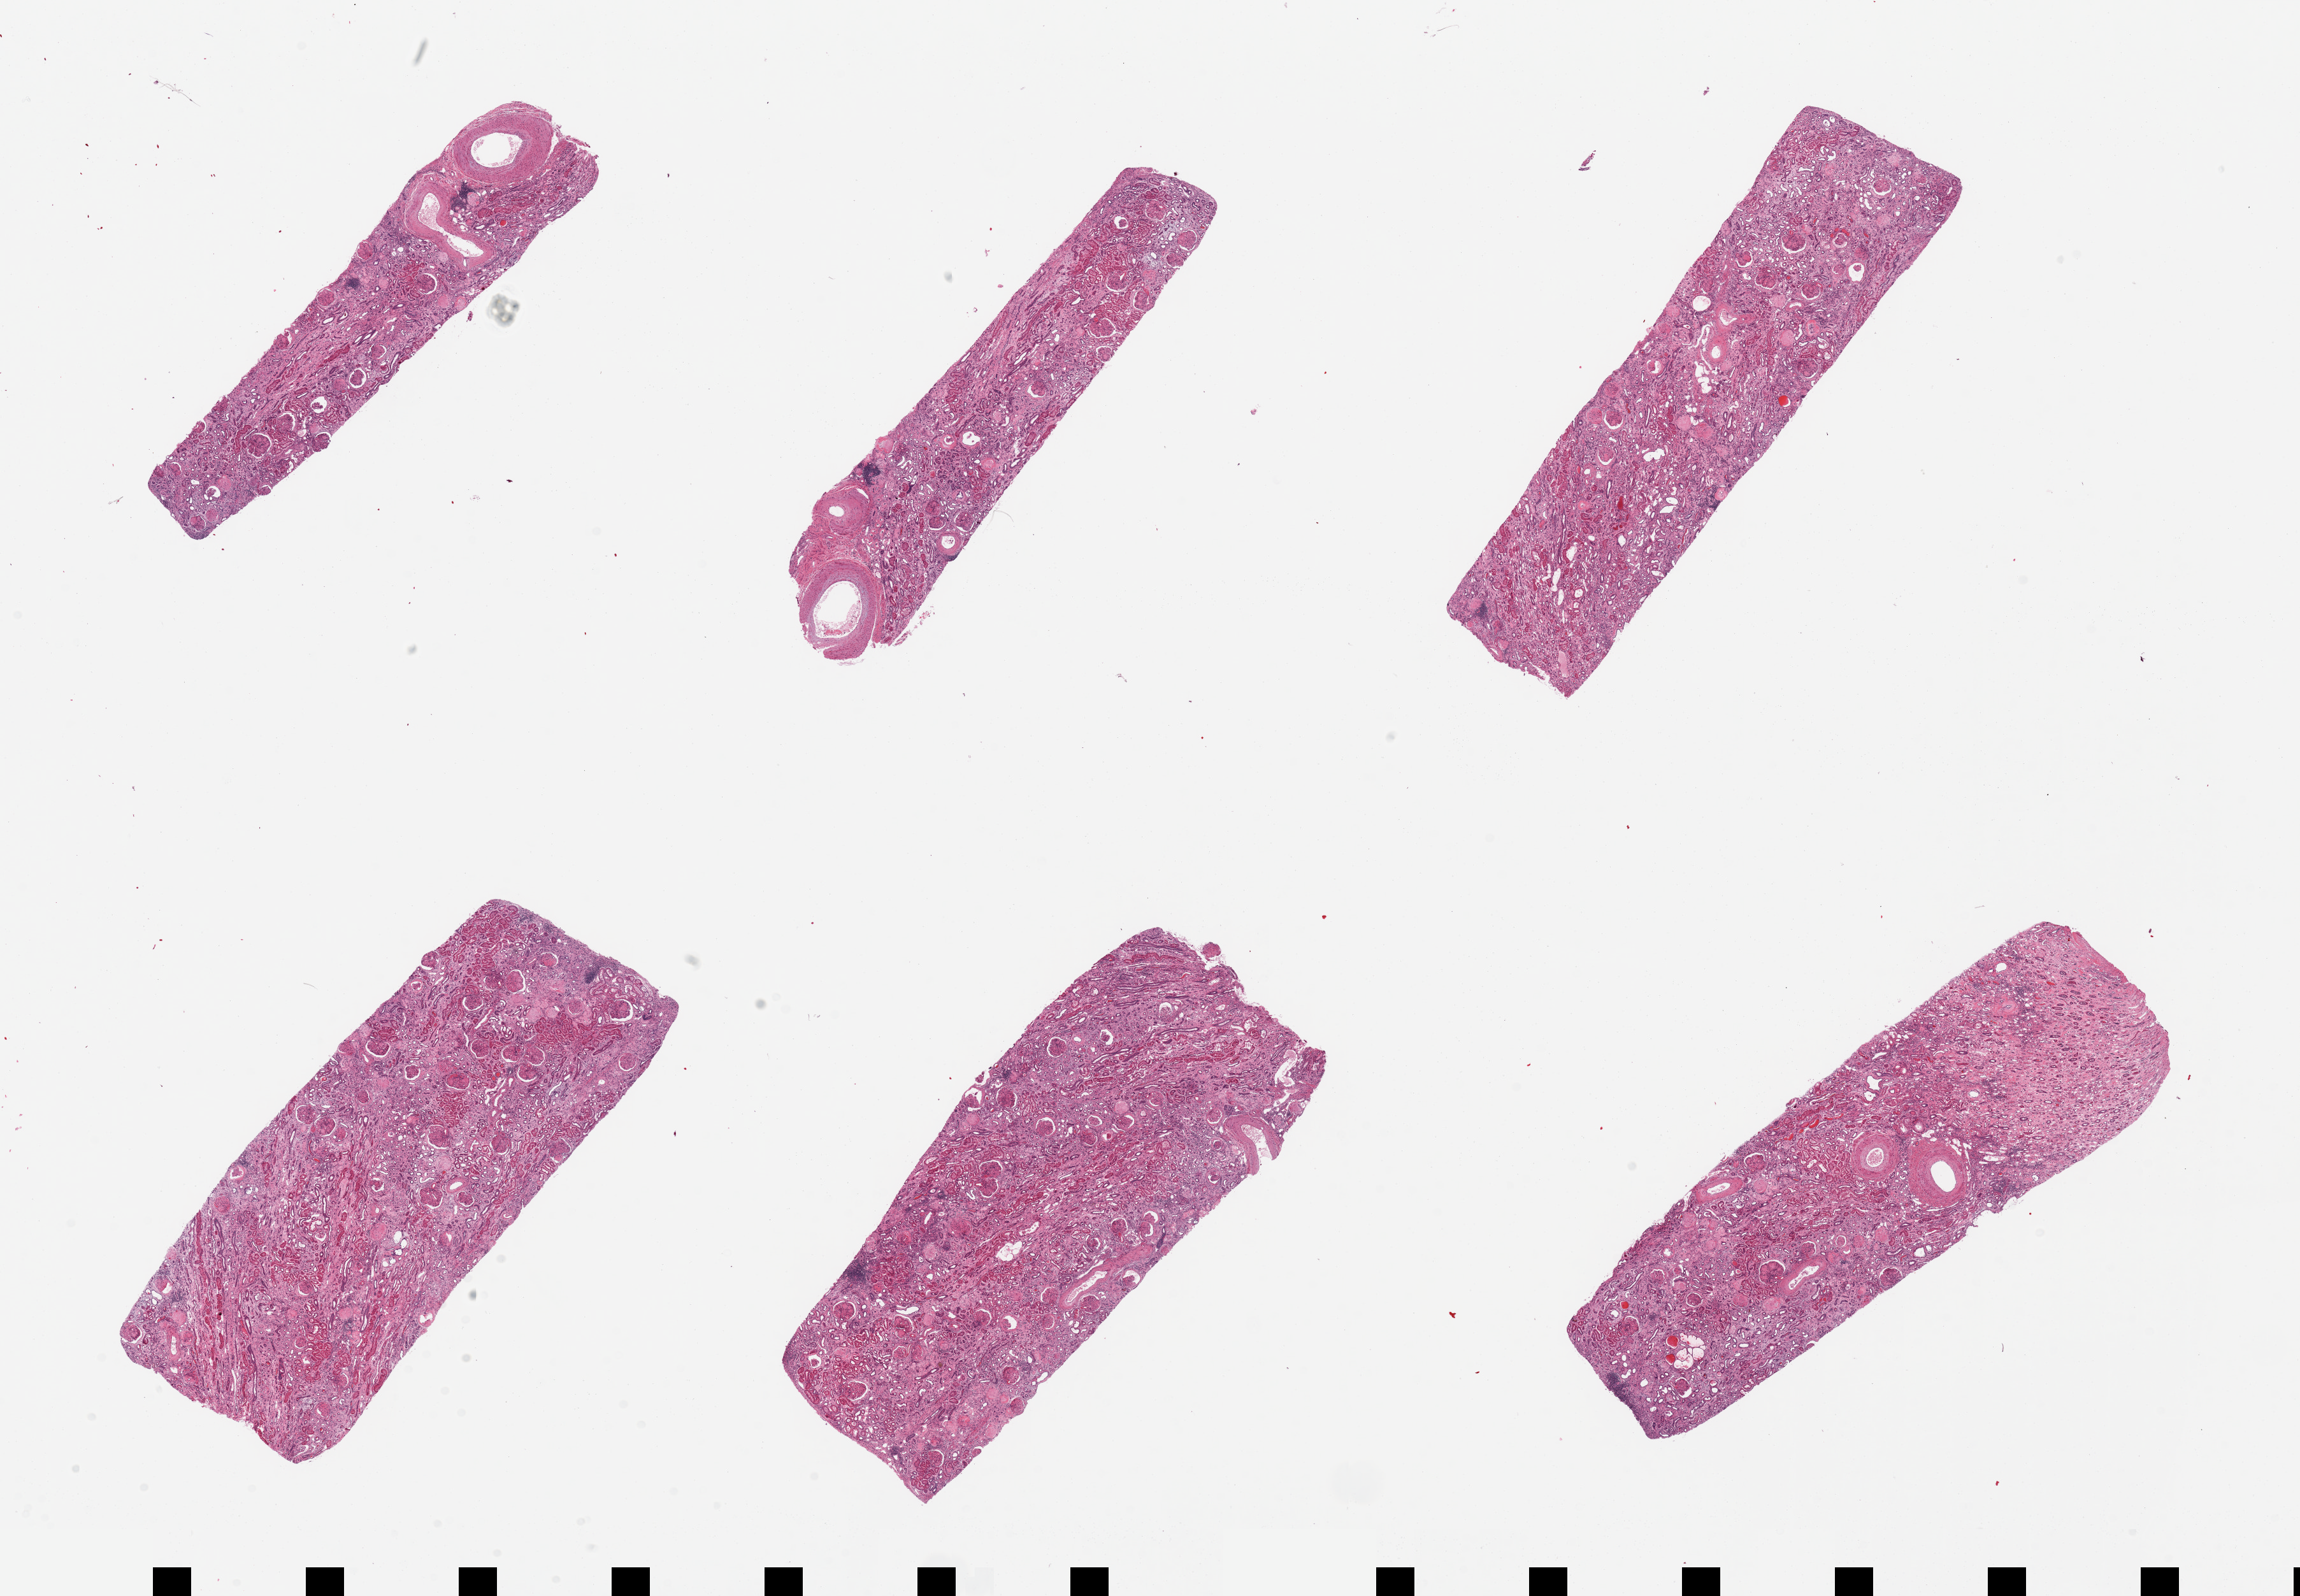
Digitized hematoxylin and eosin (H&E)-stained section — a low-resolution overview of the entire scanned area, about 28.5 x 19.8 mm, PAXgene-fixed, paraffin-embedded tissue, section of renal cortex (target tissue), tissue donor sample. Donor: male.
* pathologist's review note for this sample: 6 pieces; glomerulosclerosis typical of diabetes (no normal glomeruli); arteriolar fibrinoid degeneration typical of hypertension